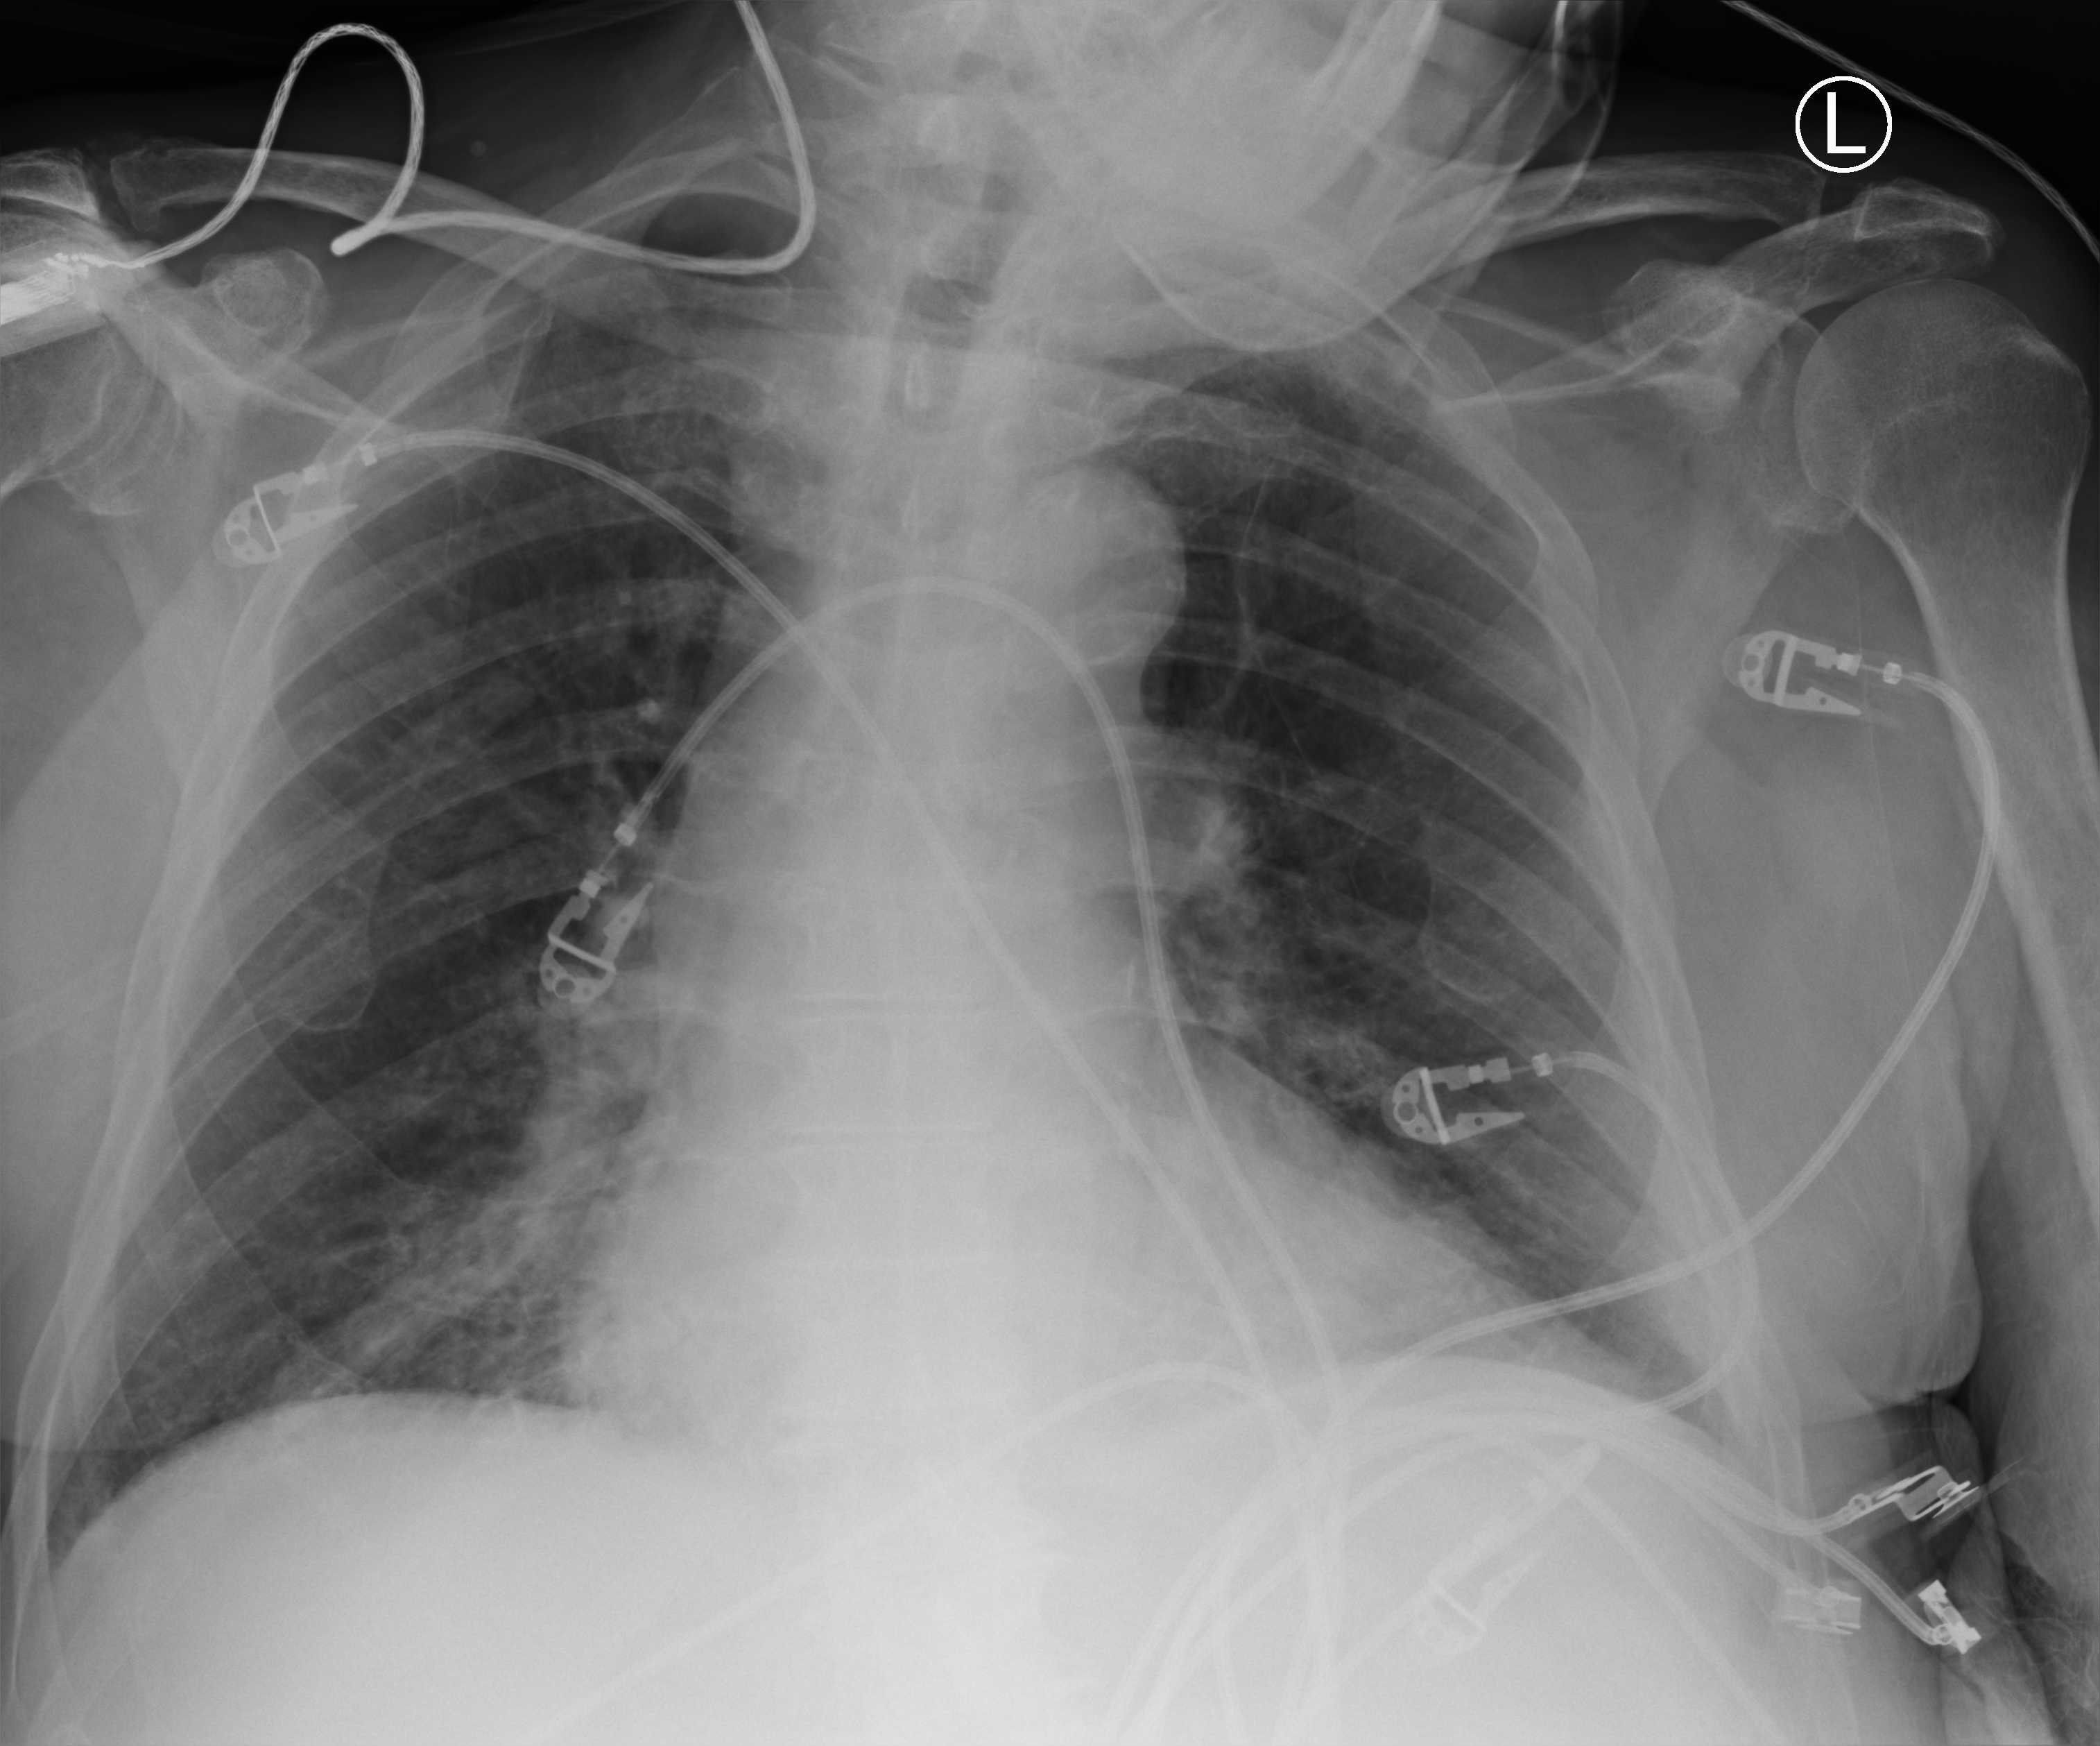
Bedside chest radiograph (computed radiography). Male patient hospitalised with COVID-19, age 75–90 years.
From the hospital-stay record, not from the radiograph (when in the stay this image was taken is not recorded):
- chronic kidney disease (admission record): no
- hypertension (admission record): yes
- length of hospital stay: 9 days